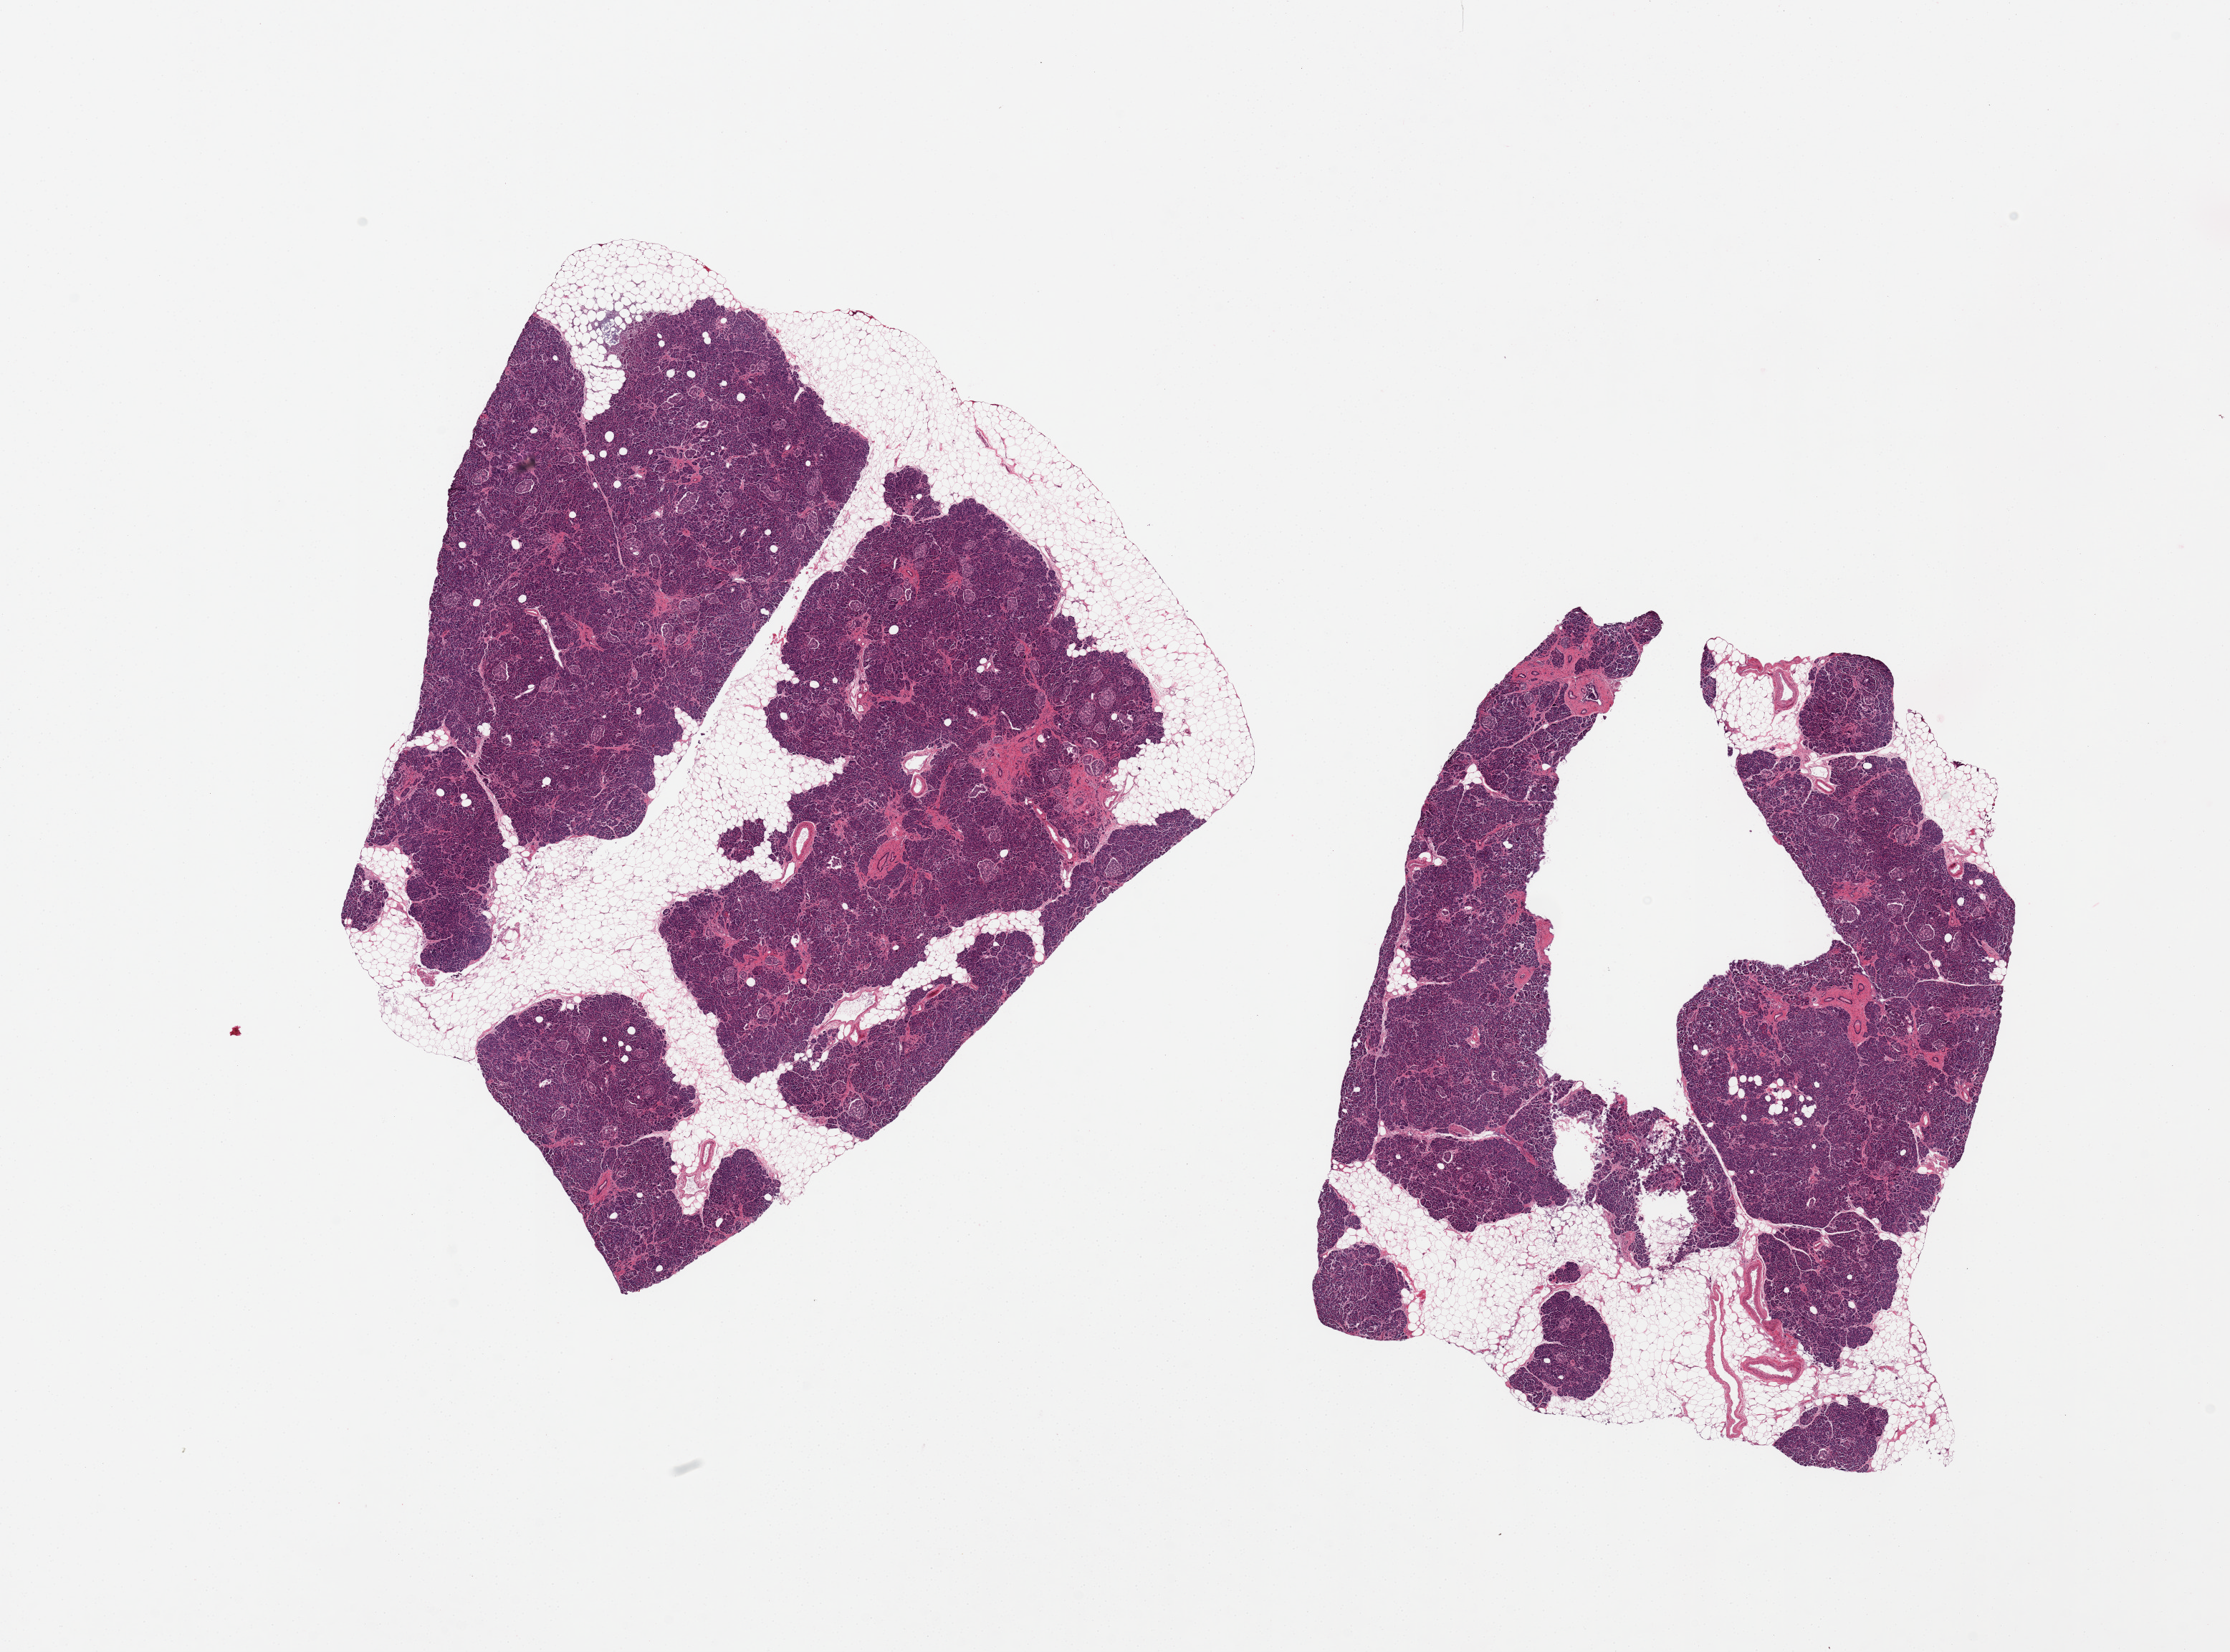
Digitized H&E-stained section — low-resolution overview of the scanned area, about 24.6 x 18.2 mm (from a 20x scan), PAXgene-fixed, paraffin-embedded tissue, section of pancreas (target tissue), tissue donor sample. Male donor.
Pathologist's review note for this sample: 2 pieces, both with up to 30% adipose tissue (internal and attached), saponification.